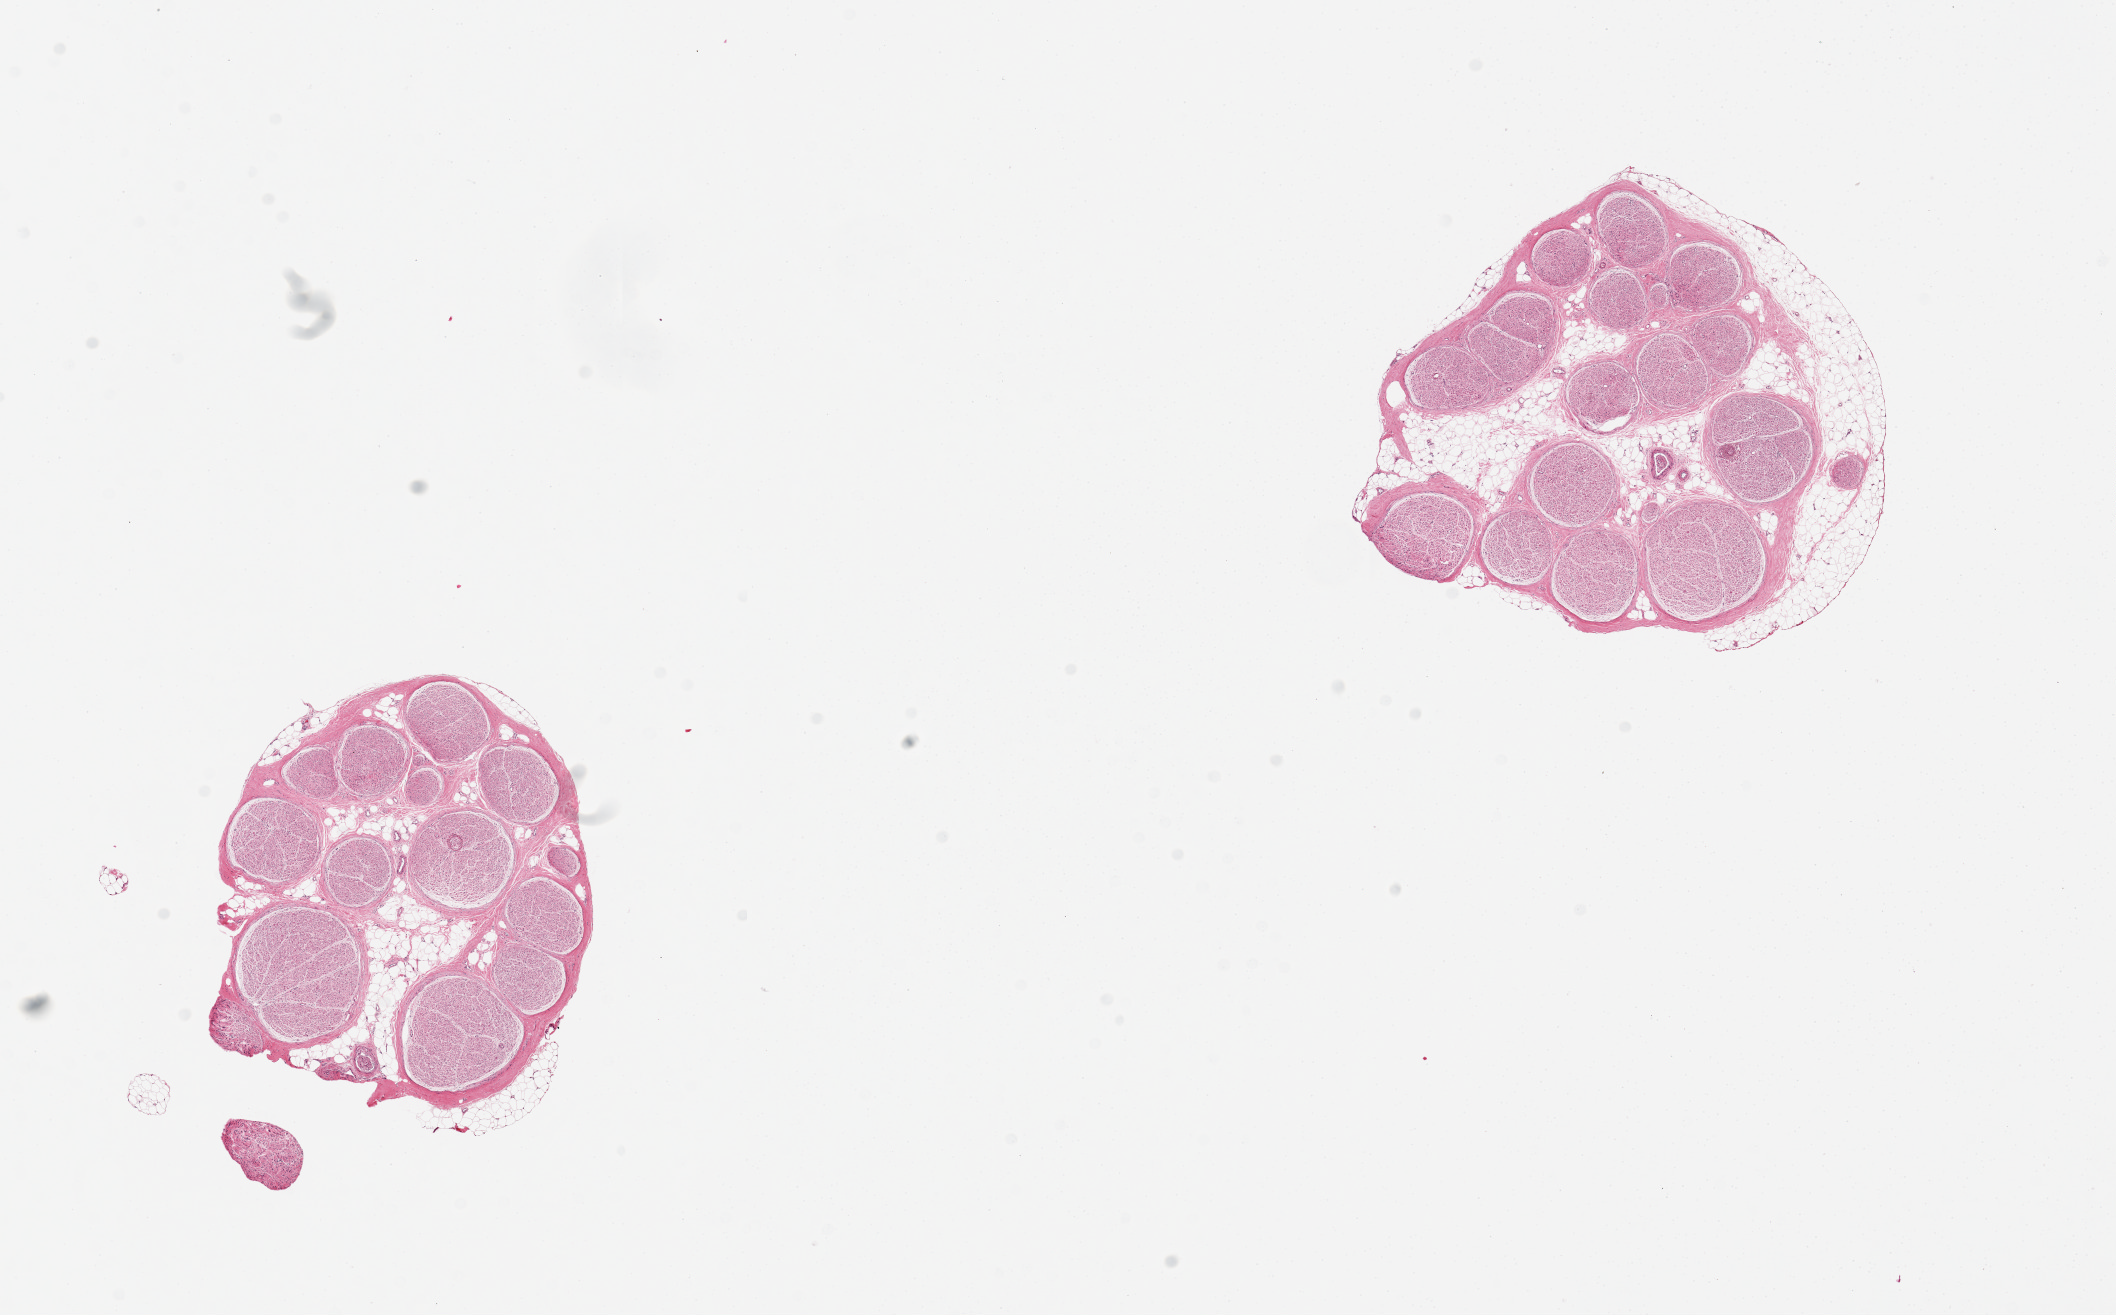
Whole-slide image, haematoxylin and eosin stain — a low-resolution overview of the entire scanned area, about 16.7 x 10.4 mm; PAXgene-fixed, paraffin-embedded tissue; target tissue: tibial nerve; tissue donor sample.
Pathologist's review note for this sample: 2 pieces, 3x3 and 4x4mm; one has partial rim of adherent fat, ~0.5mm thick.